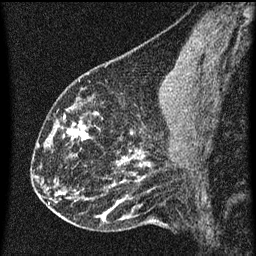
Breast MRI (dynamic contrast-enhanced), one sagittal slice. Position 26 of 60 along the scan axis. Dynamic contrast-enhanced series, image 2 of 3 at this slice position (ordered by acquisition). 1.5 T. TE 4.2 ms, TR 8 ms. 256 × 256 image matrix. Female patient, age 43 years.
Annotated regions visible in this slice (semi-automatic segmentation, software-assisted and operator-edited):
- analysis volume of interest (the breast-tissue region the enhancement analysis was run in; not a lesion): box from (x=55, y=104) to (x=101, y=149) px
- tumour enhancement mask (voxels above the 70 % enhancement threshold inside the analysis volume of interest): (x=67, y=122)–(x=89, y=141)